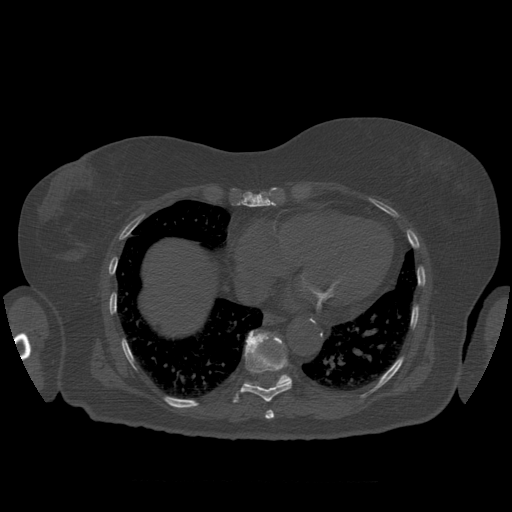
CT including the spine, one axial slice. Position 355 of 399 along the scan axis. 120 kVp. Bone window (W 1800 / L 400 HU). 512 × 512 image matrix, field of view 404 × 404 mm. Patient age 81 years. Case-level facts recorded for this patient, not image findings: primary cancer: renal.
Structures marked on this image (semi-automatic segmentation, software-assisted and operator-edited):
- T10 vertebra: box from (x=247, y=330) to (x=292, y=388) px
- T8 vertebra: (x=265, y=410)–(x=274, y=420)
- T9 vertebra: (x=234, y=331)–(x=292, y=403)